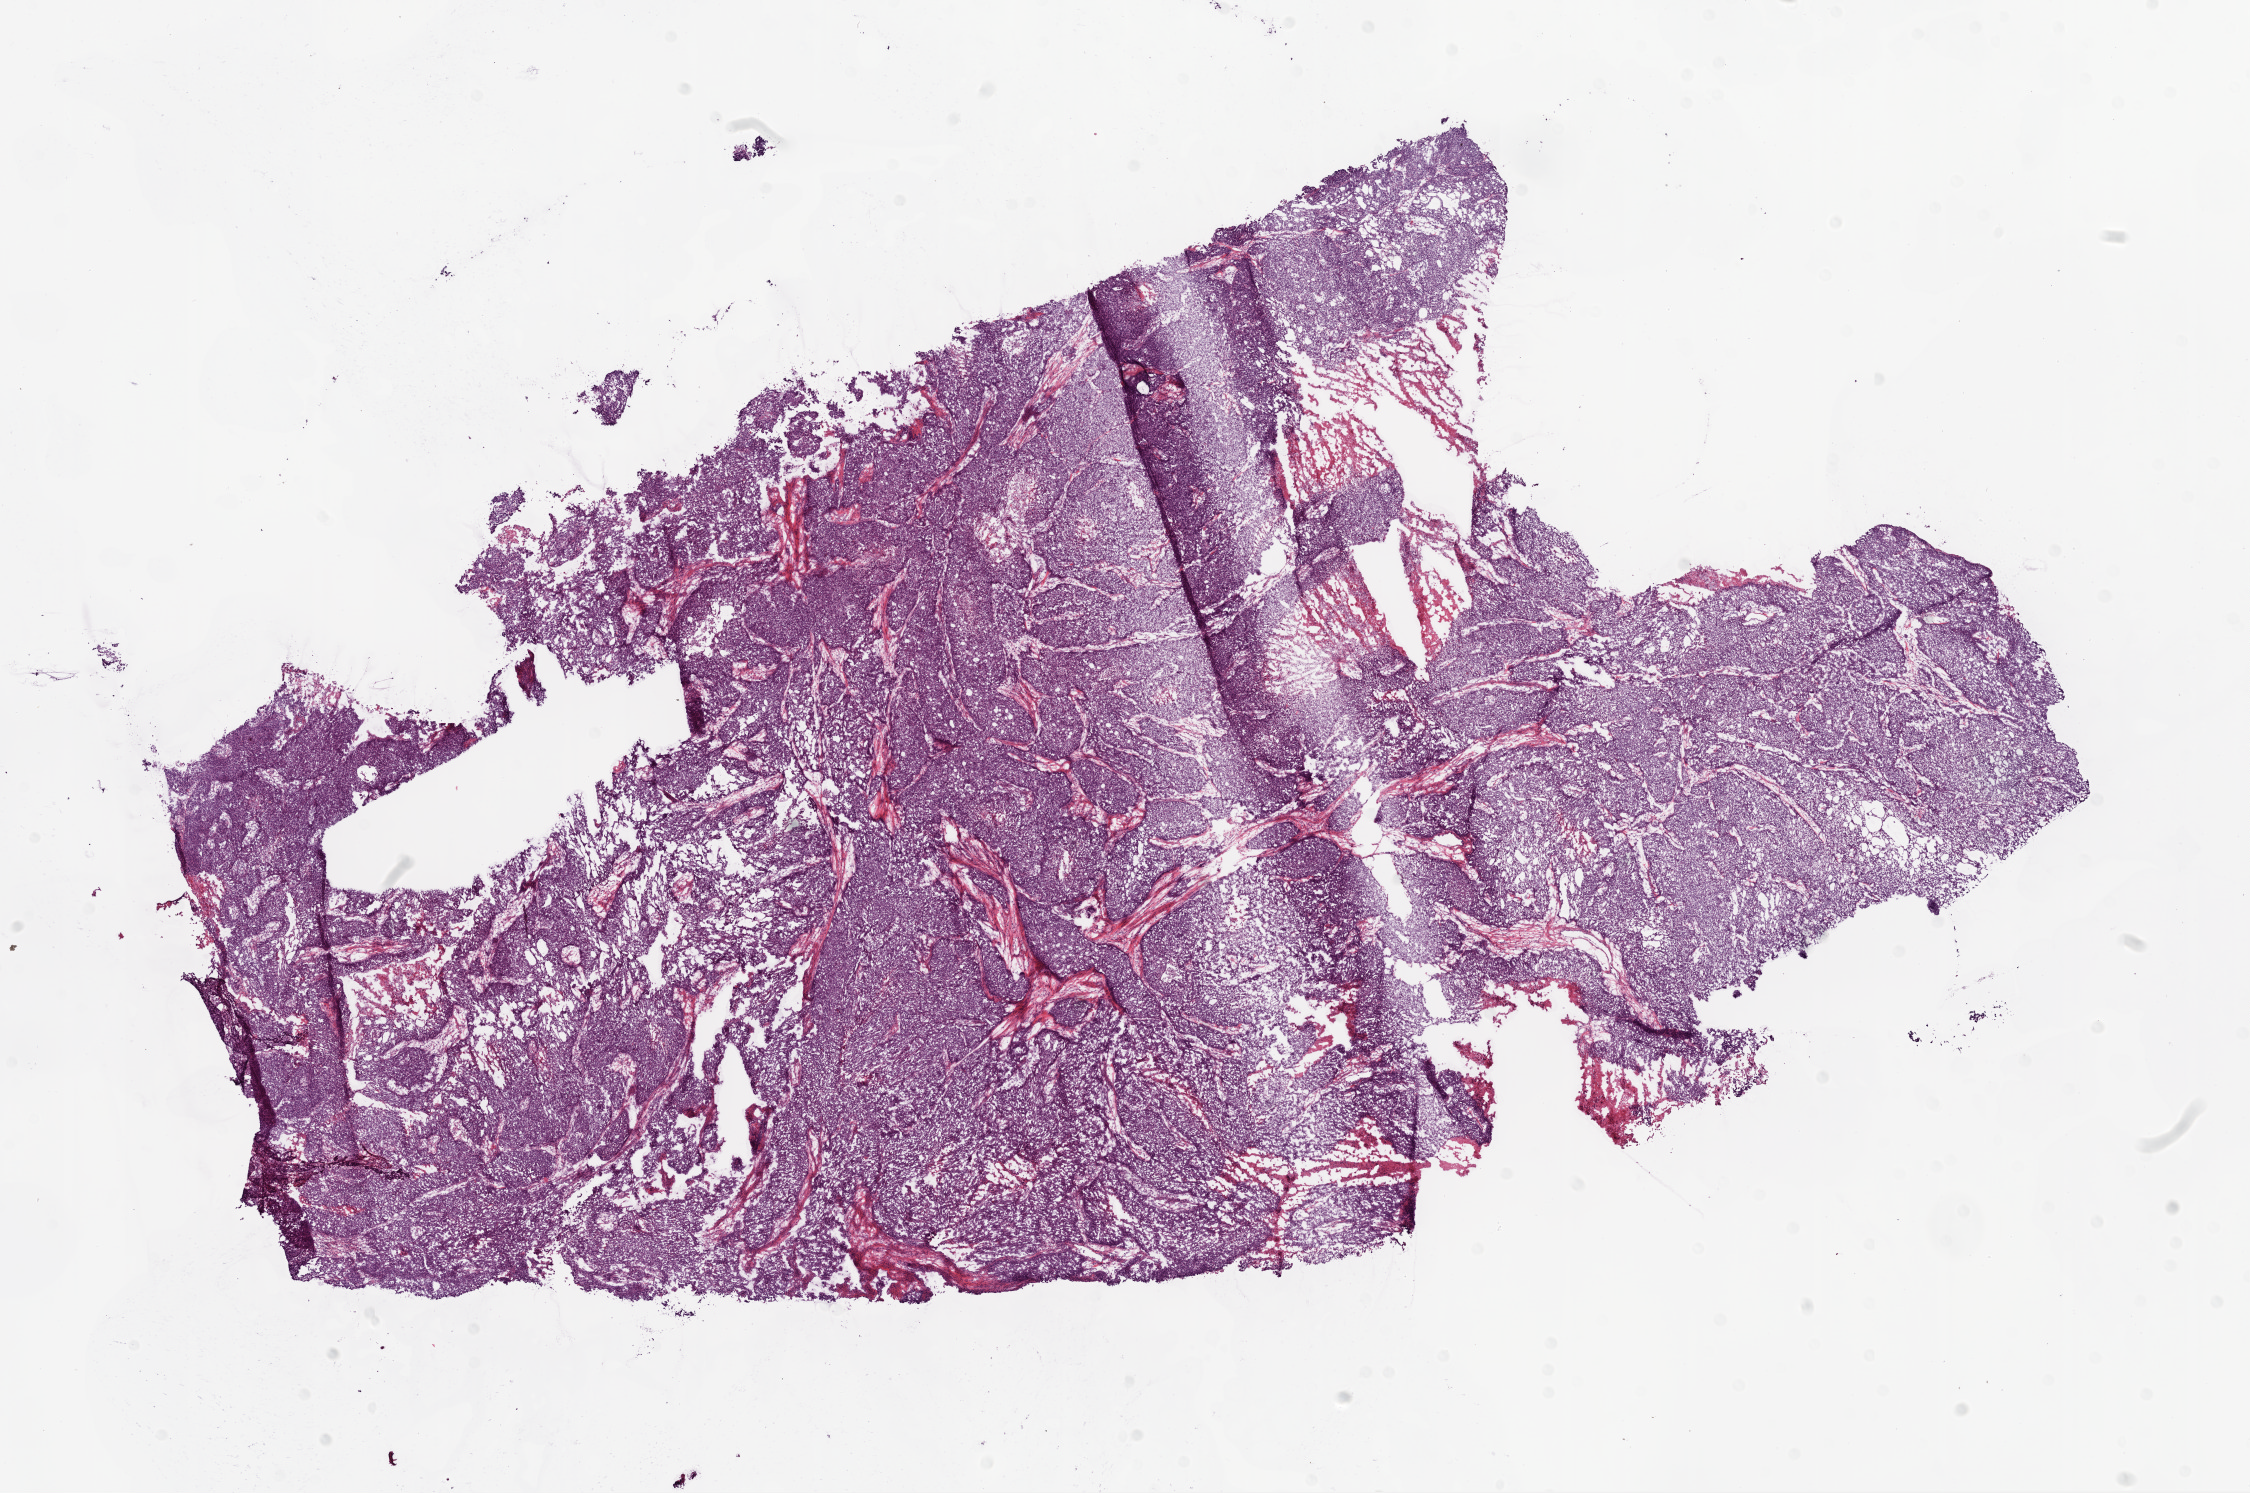
Hematoxylin and eosin (H&E) stained whole-slide image — shown as a low-resolution overview of the whole scanned area (about 18.1 x 12.0 mm); frozen section from the bottom of the tissue portion; primary tumour sample from the ovary. Female patient; age at initial diagnosis 40 years. Histologic grade: G3 (poorly differentiated). Pathologist review of this section (percent, as recorded): tumour cells 90%, tumour nuclei 97%, normal cells 5%, stromal cells 0%, necrosis 5%.
* pathologic diagnosis: Serous cystadenocarcinoma, NOS
* FIGO stage: IIIC